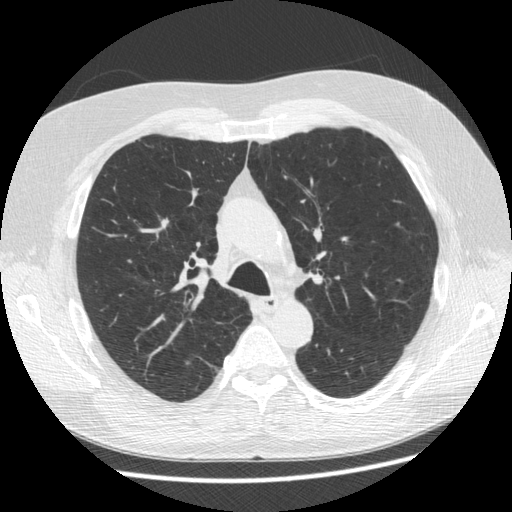
Low-dose screening chest CT, axial slice; third annual screen; lung window (W 1500 / L -600 HU); standard (soft-tissue) reconstruction kernel (STANDARD); slice 167 of 545 in the series; 512 × 512 image matrix, field of view 360 × 360 mm. Male, age 63 years at enrolment. Former smoker at enrolment.
Expert-annotated lung lesion, bounding box [x1, y1, x2, y2] px = [150, 209, 182, 238]. The screening reader recorded 2 non-calcified nodules or masses ≥4 mm on this exam (right upper lobe, left upper lobe); which of them this box marks is not recorded. Lung cancer was diagnosed 342 days after this screen: adenocarcinoma, NOS, right upper lobe, stage IIA (AJCC 6th edition), 8 mm at pathology.